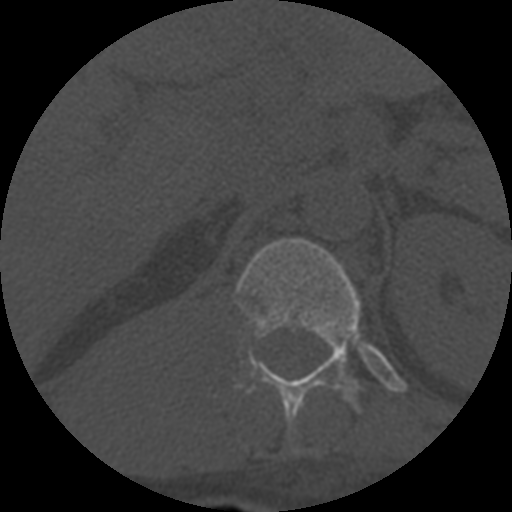
CT including the spine, one axial slice; position 313 of 708 along the scan axis; one of 3 acquisitions stored at this slice position; bone window (W 1800 / L 400 HU); 1.25 mm slice thickness; 512 × 512 image matrix, field of view 160 × 160 mm. Patient age 55 years. From the clinical record (not read from this slice): primary cancer: colon; vertebrae with lytic lesions (as recorded): T12, L1, L5.
Outlined on this slice (semi-automatic segmentation, software-assisted and operator-edited):
- T12 vertebra: box from (x=236, y=238) to (x=361, y=440) px